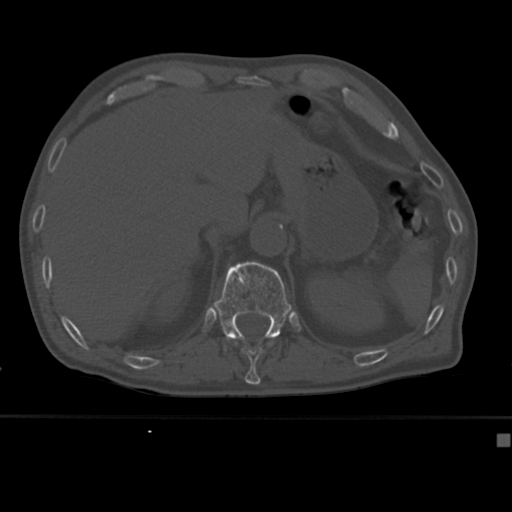
CT including the spine, one axial slice. 120 kVp. Bone window (W 1800 / L 400 HU). 1.5 mm slice thickness. 512 × 512 image matrix. Patient: male, 64 years. Case-level facts recorded for this patient, not image findings: primary cancer: uterus.
Structures marked on this image (semi-automatic segmentation, software-assisted and operator-edited):
- T11 vertebra: bounding box <235,342,272,382> (left, top, right, bottom; pixels)
- T12 vertebra: <214,261,292,351>